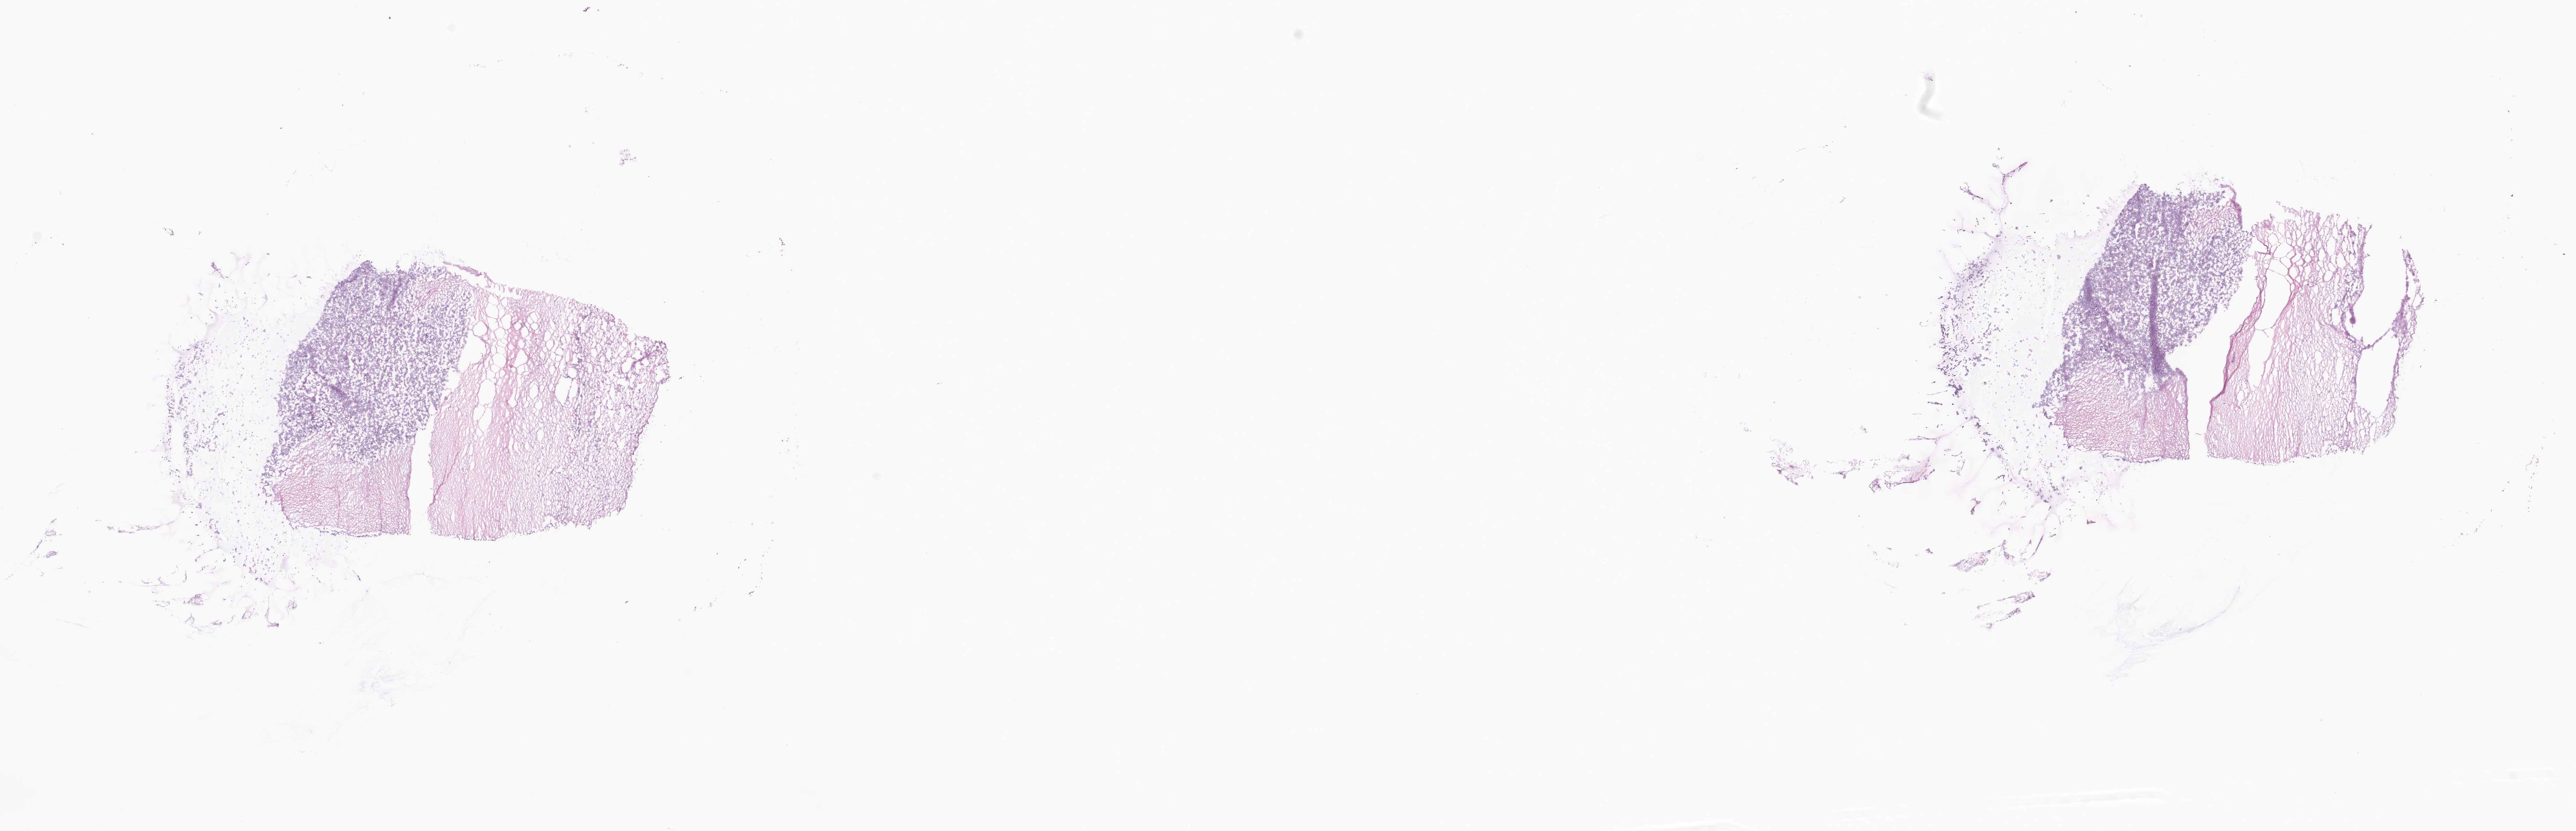
Whole-slide image, H&E stain, a low-resolution overview of the entire scanned area, about 31.1 x 10.0 mm. Frozen section. Specimen: metastatic tumor tissue. Patient sex: female. Slide review estimates, as recorded: tumor cells 40%, tumor nuclei 76%, stromal cells 0%, necrosis 5%, normal cells 55%. Infiltration values recorded for this section: lymphocyte infiltration 3%, monocyte infiltration 0%, neutrophil infiltration 0%.
• patient diagnosis (primary): Serous surface papillary carcinoma